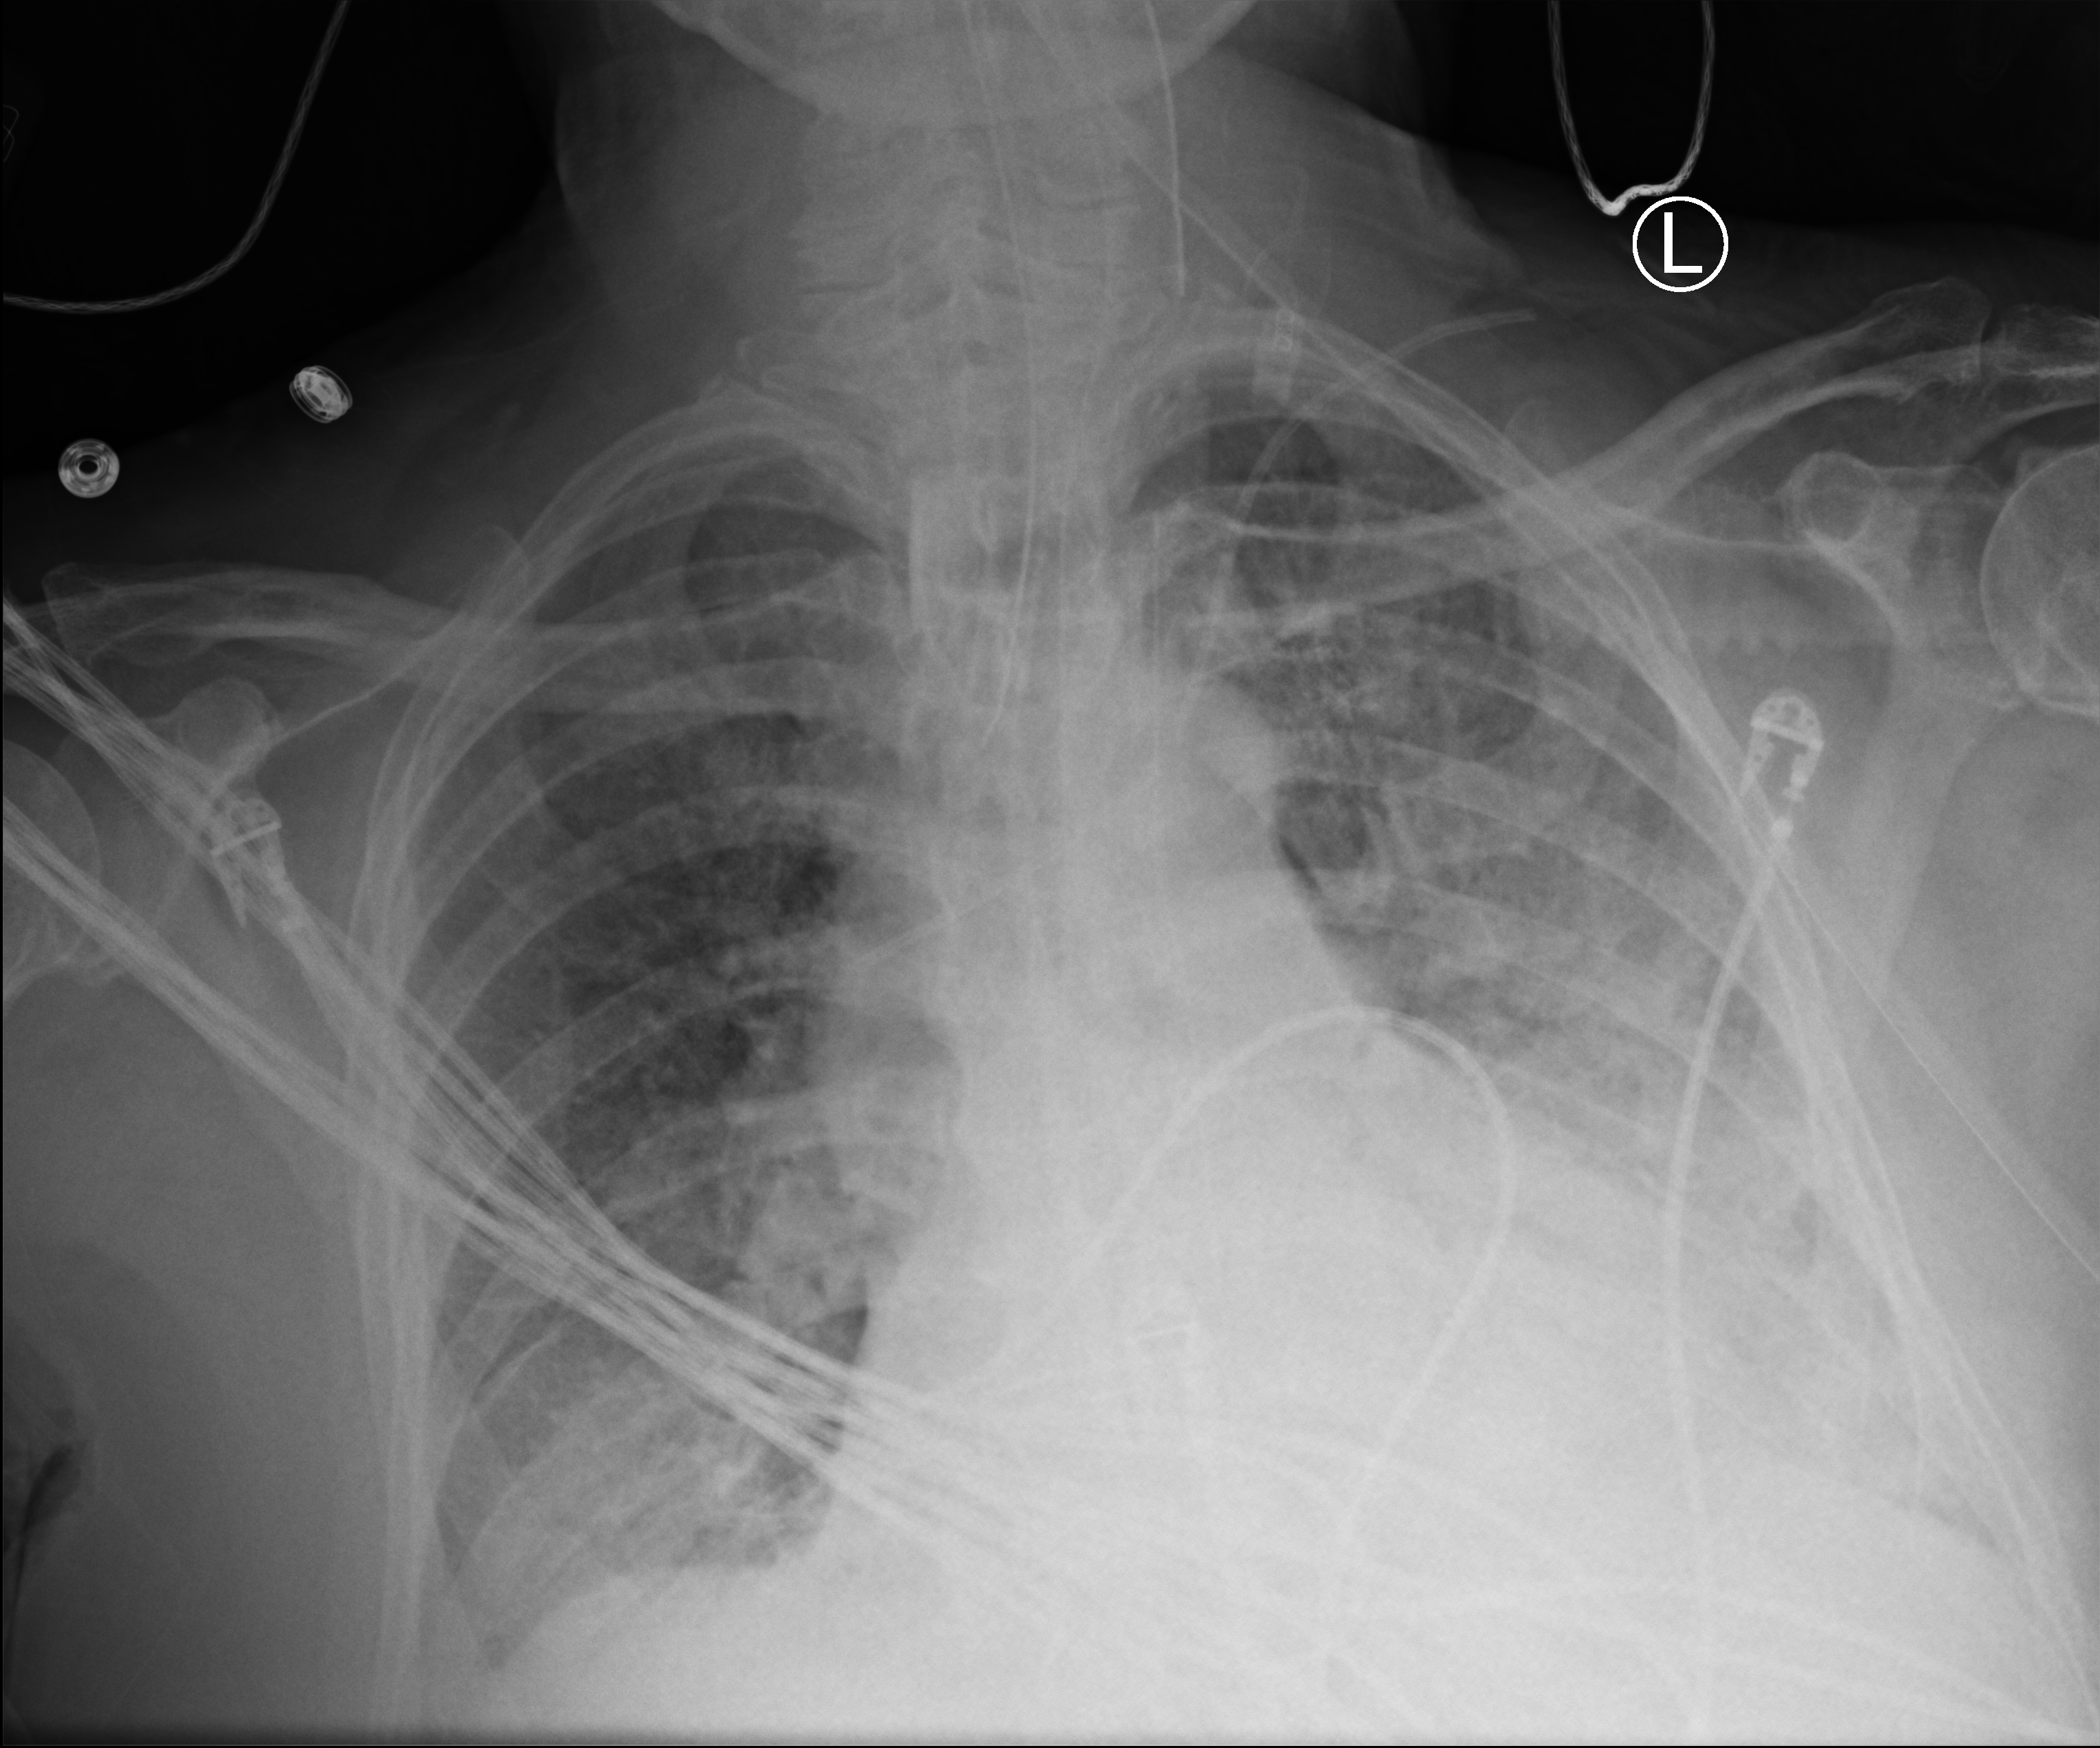
Portable chest radiograph; anteroposterior (AP) projection. Male patient hospitalised with COVID-19, age 75–90 years.
Admission-level facts for this patient (not findings on this image; timing relative to this image not recorded): hypertension (admission record): yes.